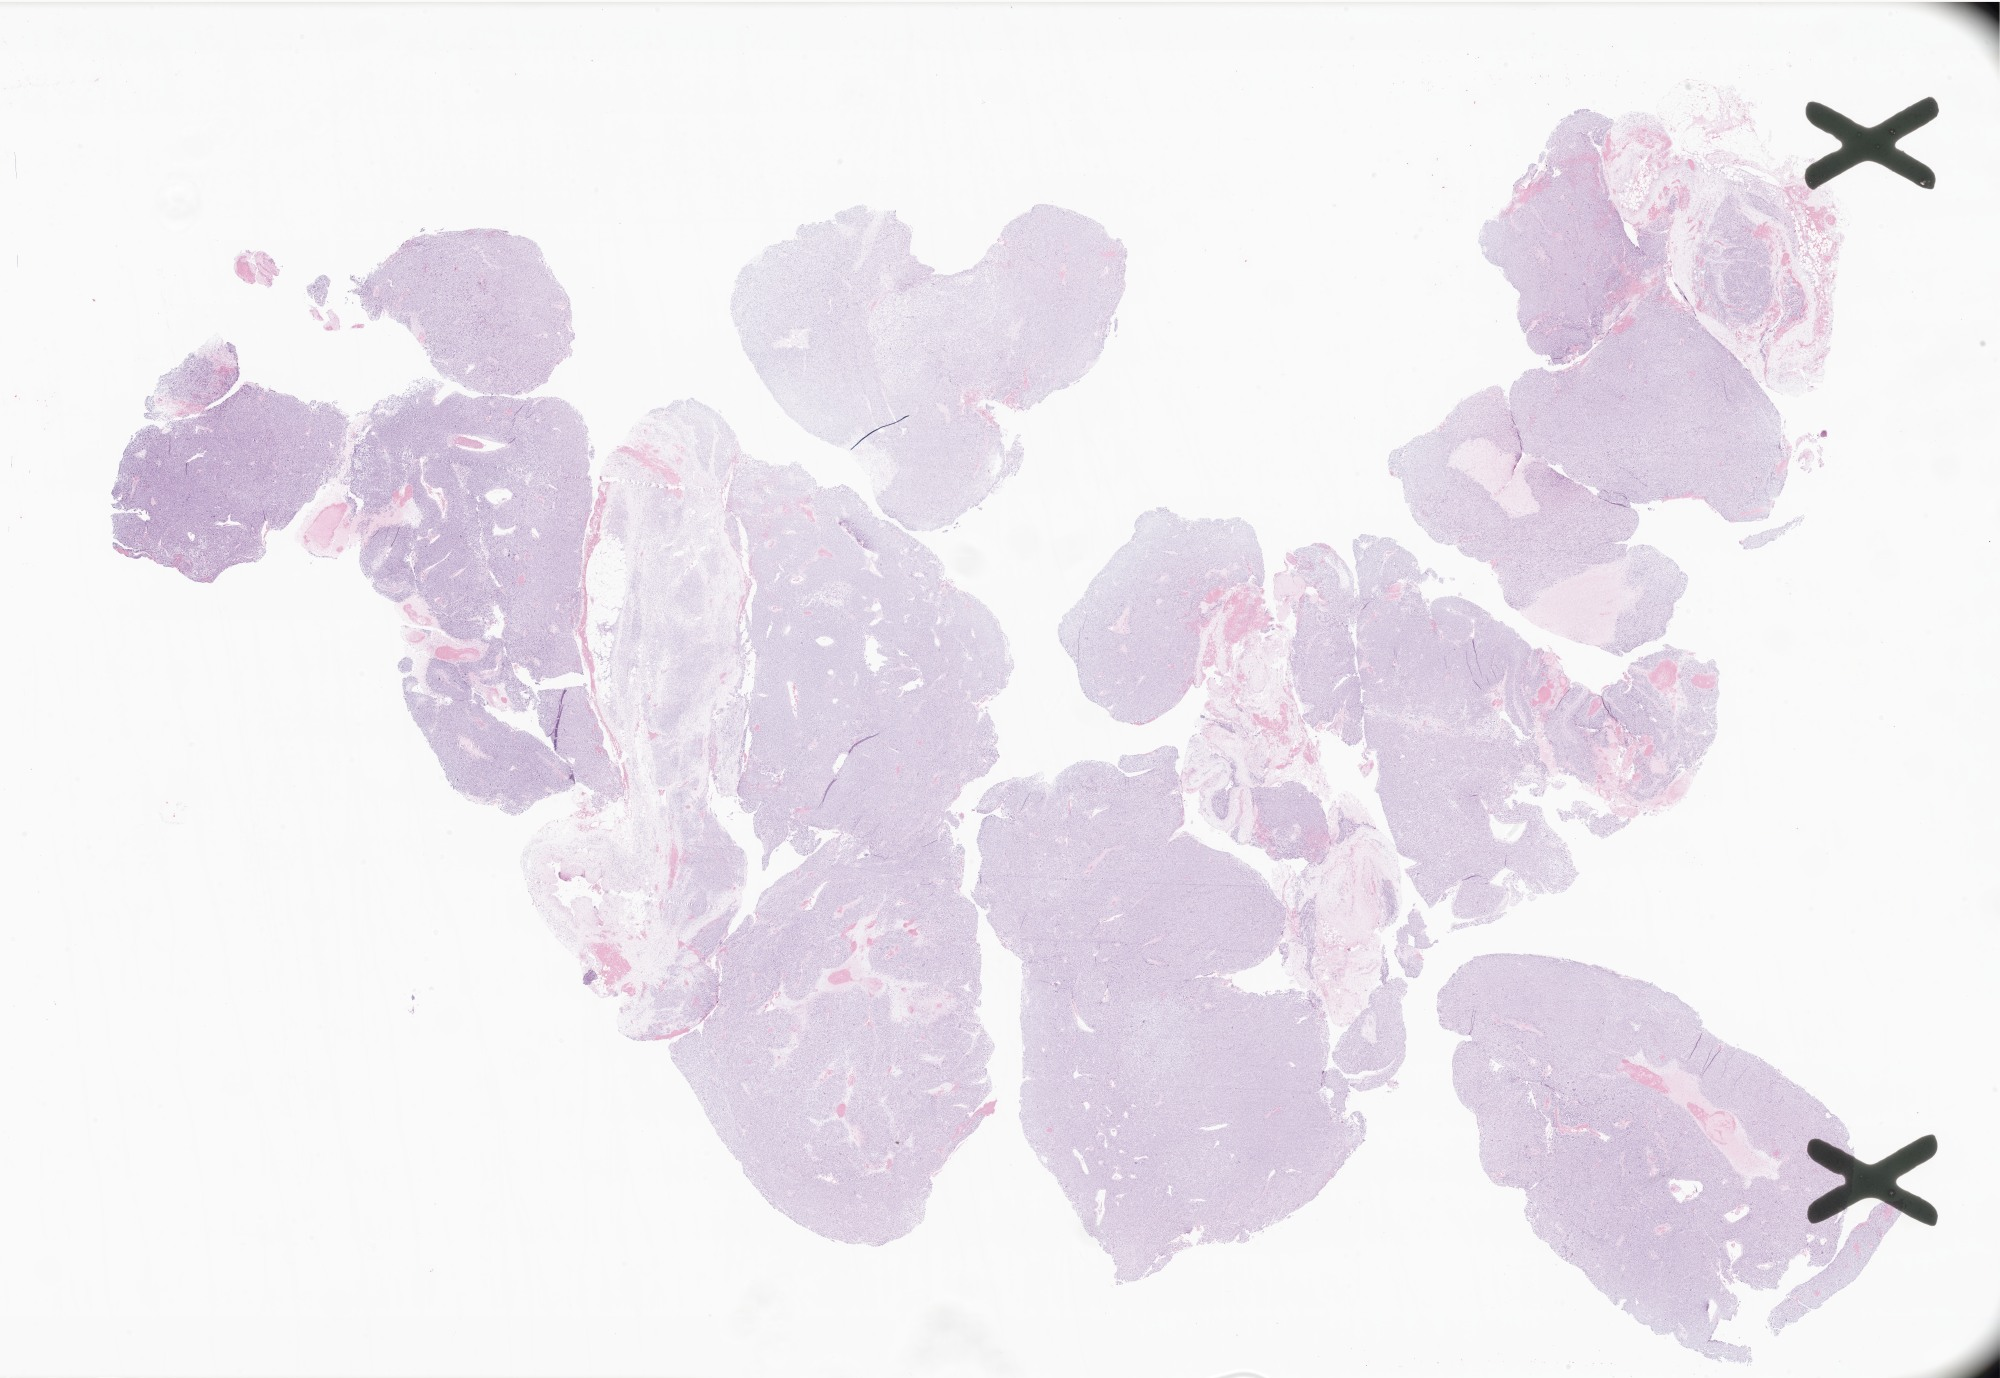
Digitized haematoxylin and eosin-stained section of tumor tissue from the orbit — low-resolution overview of the scanned area, about 33.7 x 23.2 mm; formalin-fixed, paraffin-embedded (FFPE) tissue. Patient female; age 116 months (9 years 8 months).
Diagnosis: Rhabdomyosarcoma, NOS.